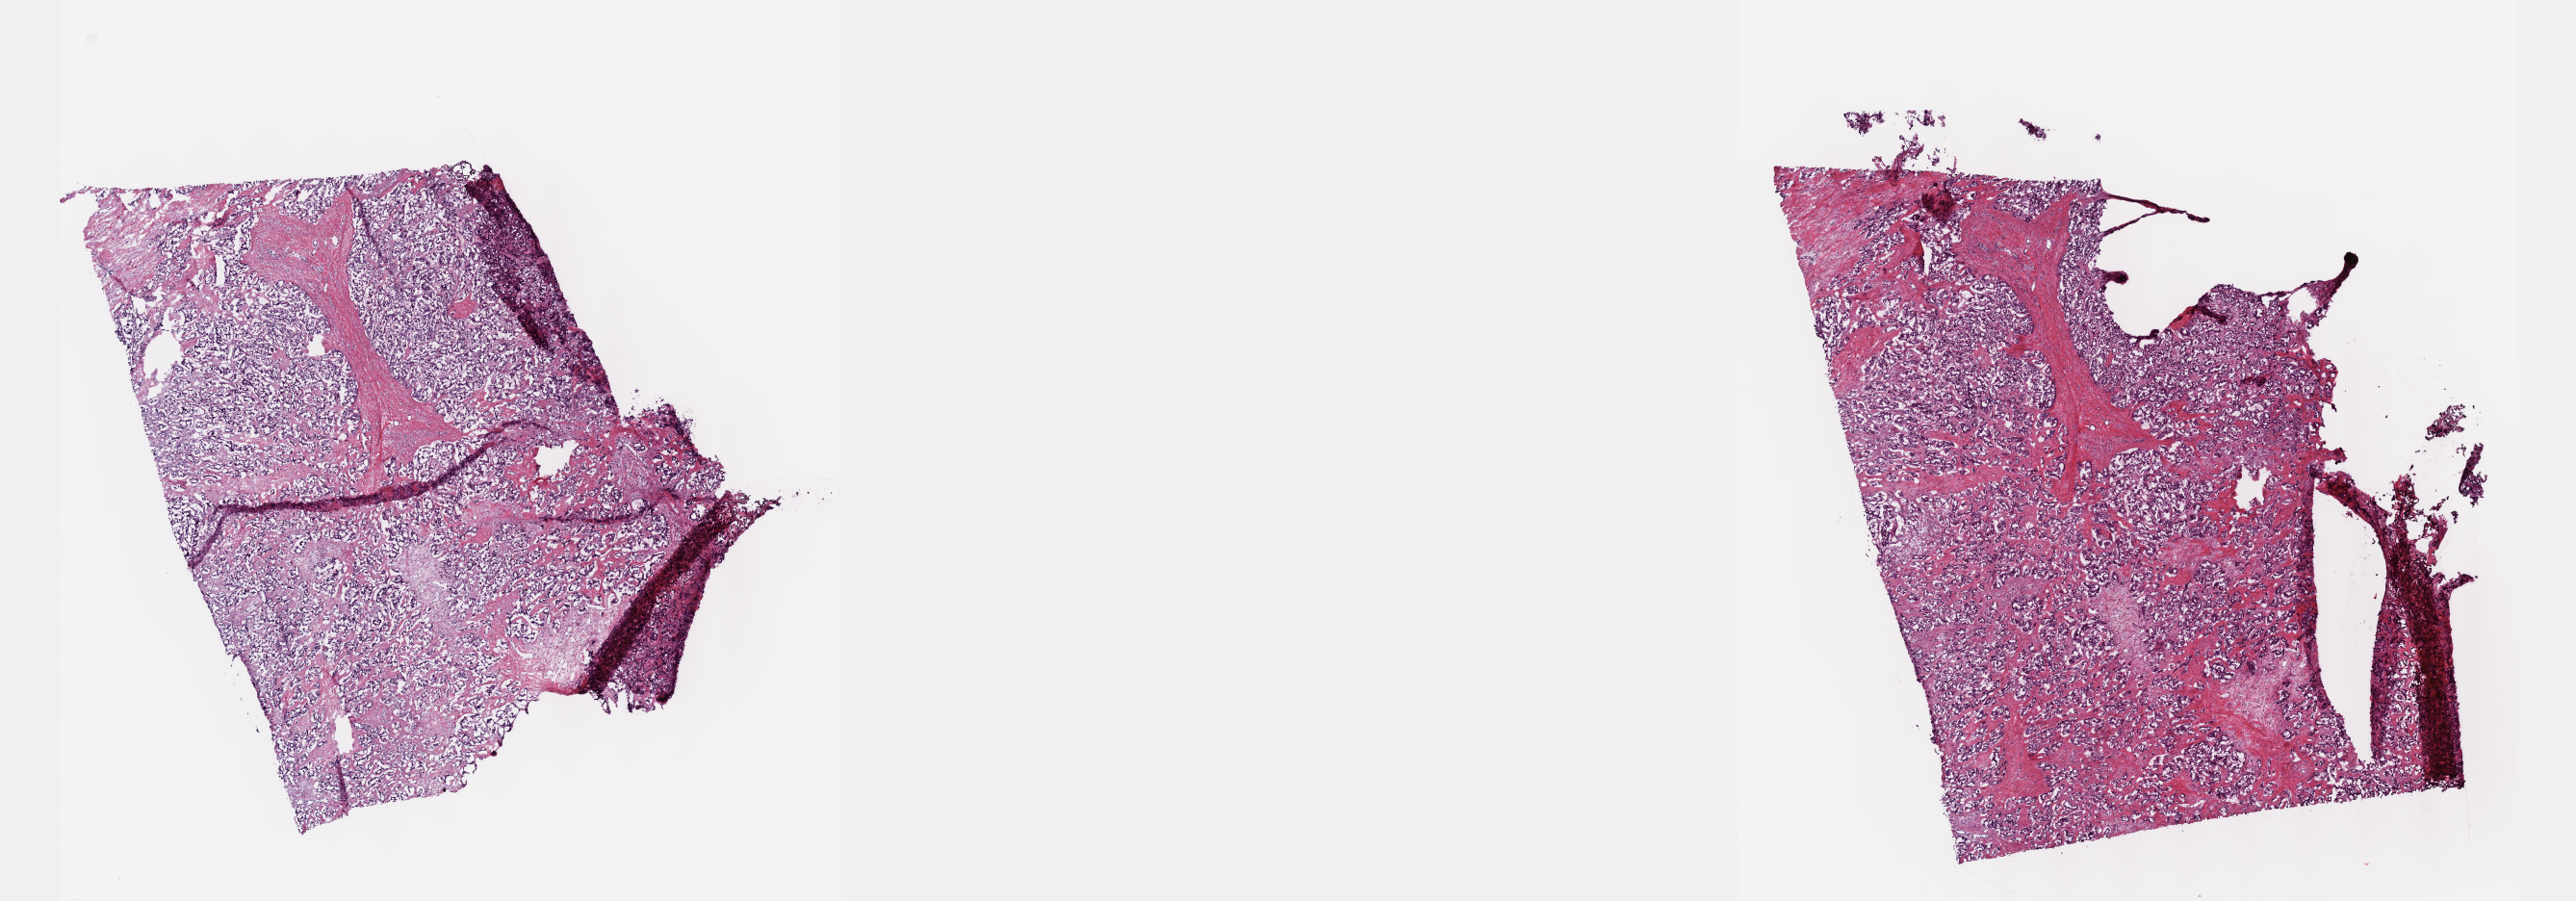
Digitized Hematoxylin and eosin (H&E) stained tissue section (whole slide), shown as a low-resolution overview of the whole scanned area (about 21.6 x 7.6 mm). Frozen section from the top of the tissue portion. Primary tumour sample from the liver. Female patient; age at initial diagnosis 60 years. Histologic grade: G2 (moderately differentiated). Pathologist review of this section (percent, as recorded): tumour cells 40%, tumour nuclei 90%, normal cells 0%, stromal cells 59%, necrosis 1%. Inflammatory infiltration, as recorded: lymphocyte infiltration 4%, monocyte infiltration 0%, neutrophil infiltration 0%.
Histologic diagnosis: Hepatocellular carcinoma, NOS. AJCC pathologic stage: IIIA (7th edition).